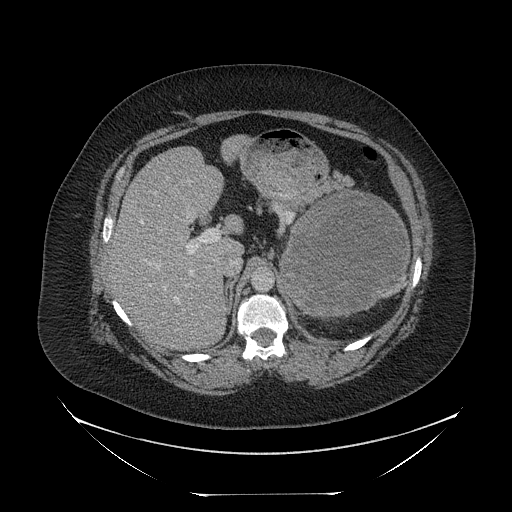
Contrast-enhanced abdominal CT, one axial slice; position 153 of 205 along the scan axis; reconstruction kernel STANDARD; 120 kVp; soft-tissue window (W 400 / L 40 HU); 2.5 mm slice thickness; 512 × 512 image matrix. Patient: female, 53 years. Case-level facts recorded for this patient, not image findings: diagnosis: adrenocortical carcinoma; tumour side: left adrenal; tumour size at pathology: 17 cm; Ki-67 index: 20 %.
Outlined on this slice (semi-automatically segmented with operator editing):
- mass: bounding box <287,193,409,317> (left, top, right, bottom; pixels)